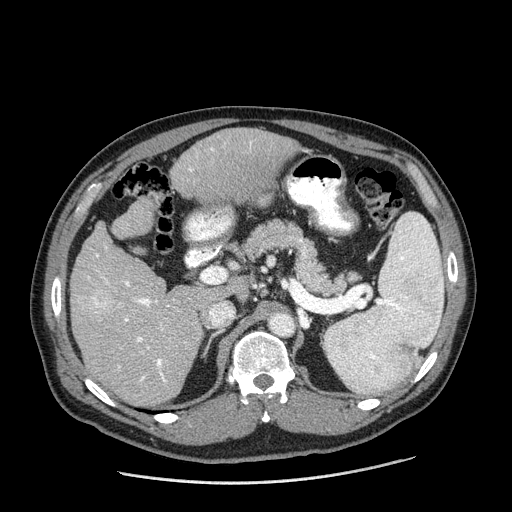
Contrast-enhanced abdominal CT (liver protocol), one axial slice. Position 105 of 198 along the scan axis. Reconstruction kernel STANDARD. 120 kVp. One of 2 acquisitions stored at this slice position. Soft-tissue window (W 400 / L 40 HU). 2.5 mm slice thickness. 512 × 512 image matrix, field of view 400 × 400 mm. Case-level facts recorded for this patient, not image findings: diagnosis: hepatocellular carcinoma (patient treated with transarterial chemoembolisation; whether this scan precedes or follows treatment is not stated here); TNM stage (as recorded): Stage-II; Child-Pugh class: A; tumour differentiation: moderately differentiated.
Outlined on this slice (semi-automatically segmented with operator editing):
- liver parenchyma outside the tumour (the mass and vessels are separate outlines, so this box may not span the whole liver): bounding box (x1, y1, x2, y2) in pixels: (70, 128, 300, 406)
- mass: (88, 287, 112, 314)
- liver vessels: (88, 143, 252, 382)